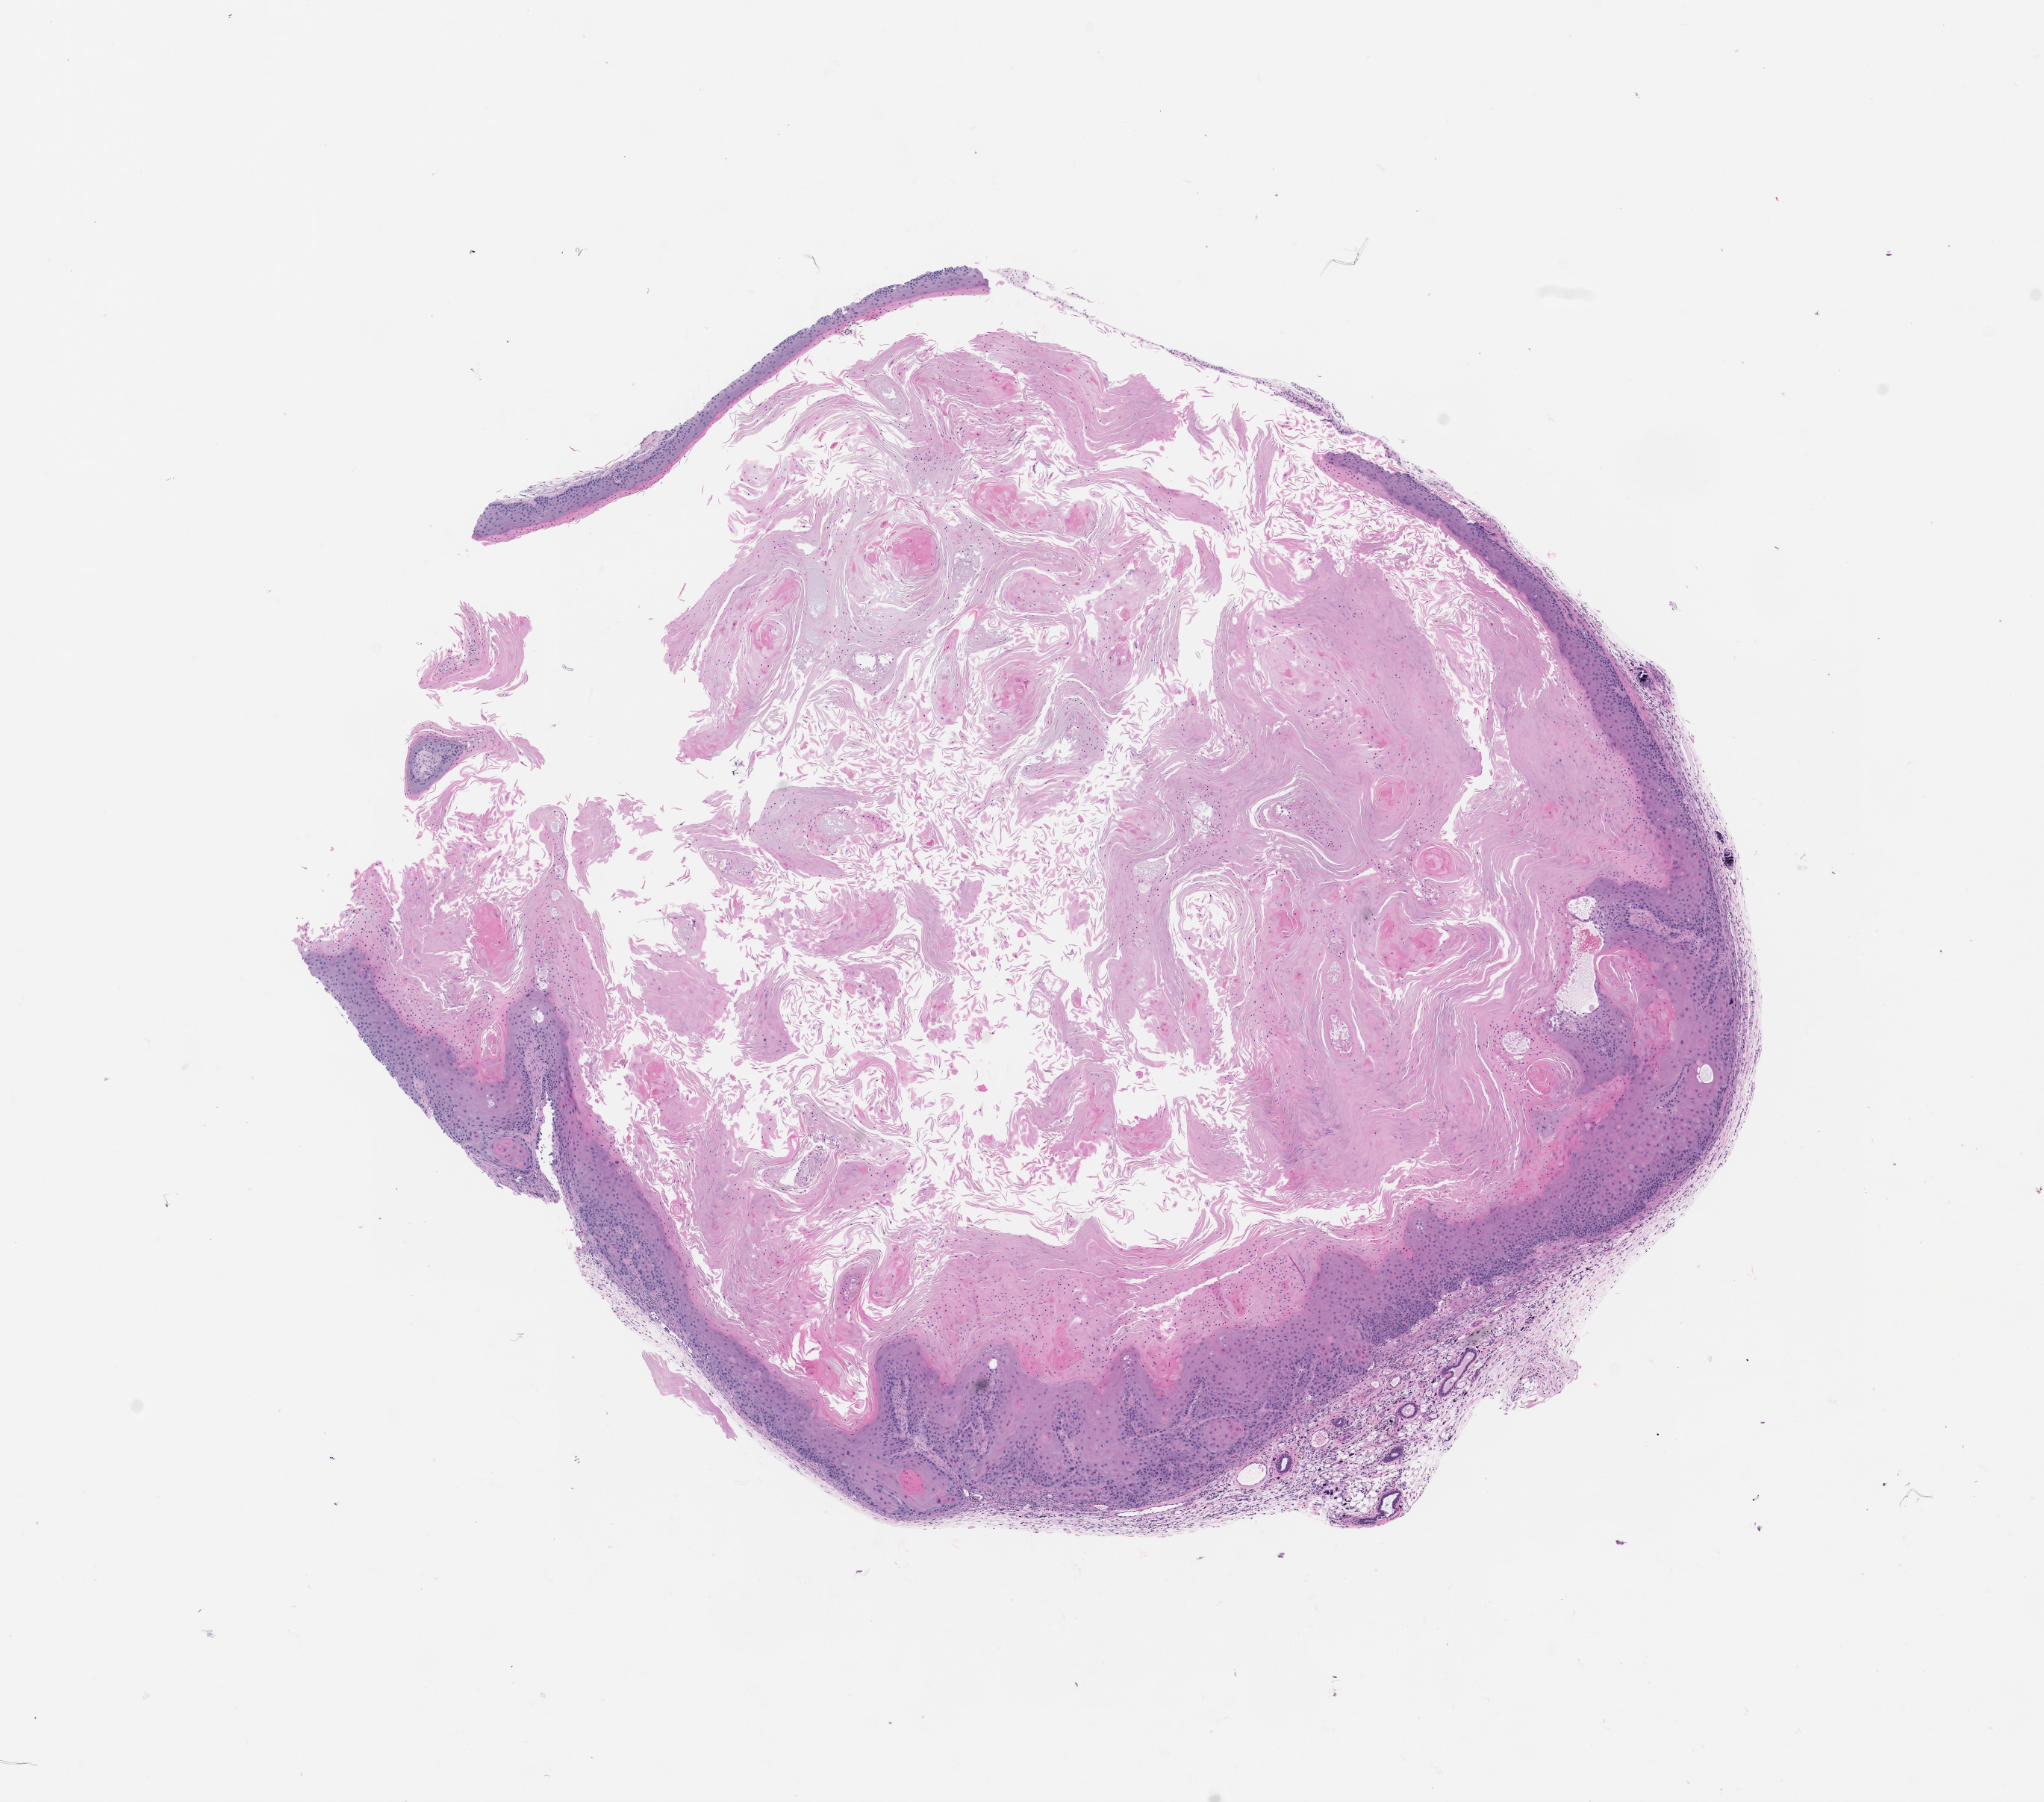
Whole-slide image, haematoxylin and eosin: patient-derived xenograft (human tumor grown in a mouse), passage 0 — a low-resolution overview of the entire scanned area, about 11.0 x 9.7 mm; formalin-fixed paraffin-embedded section; tumor site category: oral soft tissue.
Originating patient diagnosis: Head and Neck Squamous Cell Carcinoma.